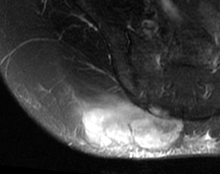
MRI of an extremity soft-tissue mass, one axial slice; slice 40 of 63 in the series (ordered by position); T2-weighted fat-saturated; MR volume resampled by the dataset authors to the PET/CT grid (not the native acquisition matrix); 3.27 mm slice thickness; 220 × 174 image matrix, field of view 215 × 170 mm. Female patient. Case-level facts recorded for this patient, not image findings: histological type: spindle cell suggestive of myxofibrosarcoma; grade: intermediate; site of the primary tumour: right buttock.
Structures marked on this image (expert contour drawn on MRI and transferred to this co-registered scan by the dataset authors):
- gross tumour volume (mass): box from (x=79, y=104) to (x=183, y=153) px